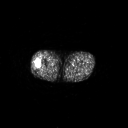
FDG PET of an extremity soft-tissue mass (from a PET/CT study), one axial slice. Slice 232 of 267 in the series (ordered by position). 3.27 mm slice thickness. 128 × 128 image matrix, field of view 700 × 700 mm. Patient: male, 43 years. Case-level facts recorded for this patient, not image findings: histological type: poorly differentiated synovial sarcoma; grade: high; site of the primary tumour: right buttock.
Outlined on this slice (expert contour drawn on MRI and transferred to this co-registered scan by the dataset authors):
- gross tumour volume including surrounding oedema: bounding box <34,58,44,69> (left, top, right, bottom; pixels)
- gross tumour volume (mass): <34,59,42,69>